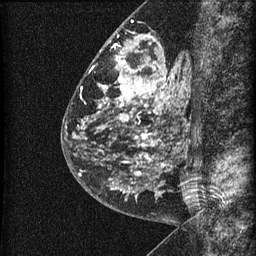
Breast MRI (dynamic contrast-enhanced), one sagittal slice. Slice 26 of 60 in the series (ordered by position). Dynamic contrast-enhanced series, image 2 of 3 at this slice position (ordered by acquisition). 1.5 T. TE 4.2 ms, TR 22.7 ms. 256 × 256 image matrix, field of view 180 × 180 mm. Patient: female, 48 years. From the clinical record (not read from this slice): setting: breast cancer imaged before/during neoadjuvant chemotherapy; receptor status: triple-negative.
Structures marked on this image (semi-automatically segmented with operator editing):
- analysis volume of interest (the breast-tissue region the enhancement analysis was run in; not a lesion): bounding box [x1, y1, x2, y2] px = [81, 23, 186, 202]
- tumour enhancement mask (voxels above the 90 % enhancement threshold inside the analysis volume of interest): [82, 35, 175, 195]